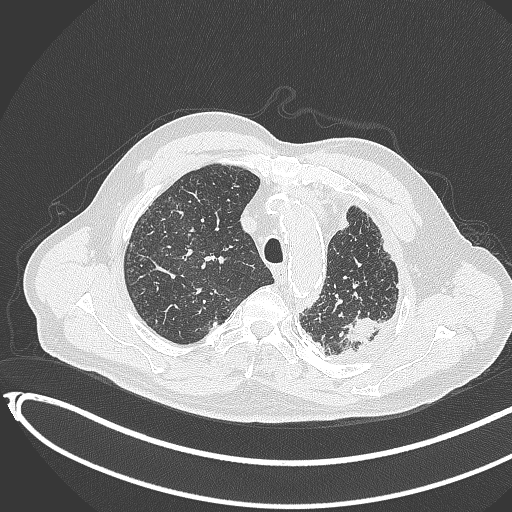
Chest CT, one axial slice; slice 341 of 451 in the series (ordered by position); 120 kVp; lung window (W 1500 / L -600 HU); 1 mm slice thickness; 512 × 512 image matrix, field of view 400 × 400 mm. Male patient, age 78 years. From the clinical record (not read from this slice): clinical TNM (as recorded): T1c N0 M1.
Outlined on this slice (bounding box drawn by a radiologist):
- lung tumour (recorded histology: adenocarcinoma): bounding box <338,313,390,346> (left, top, right, bottom; pixels)